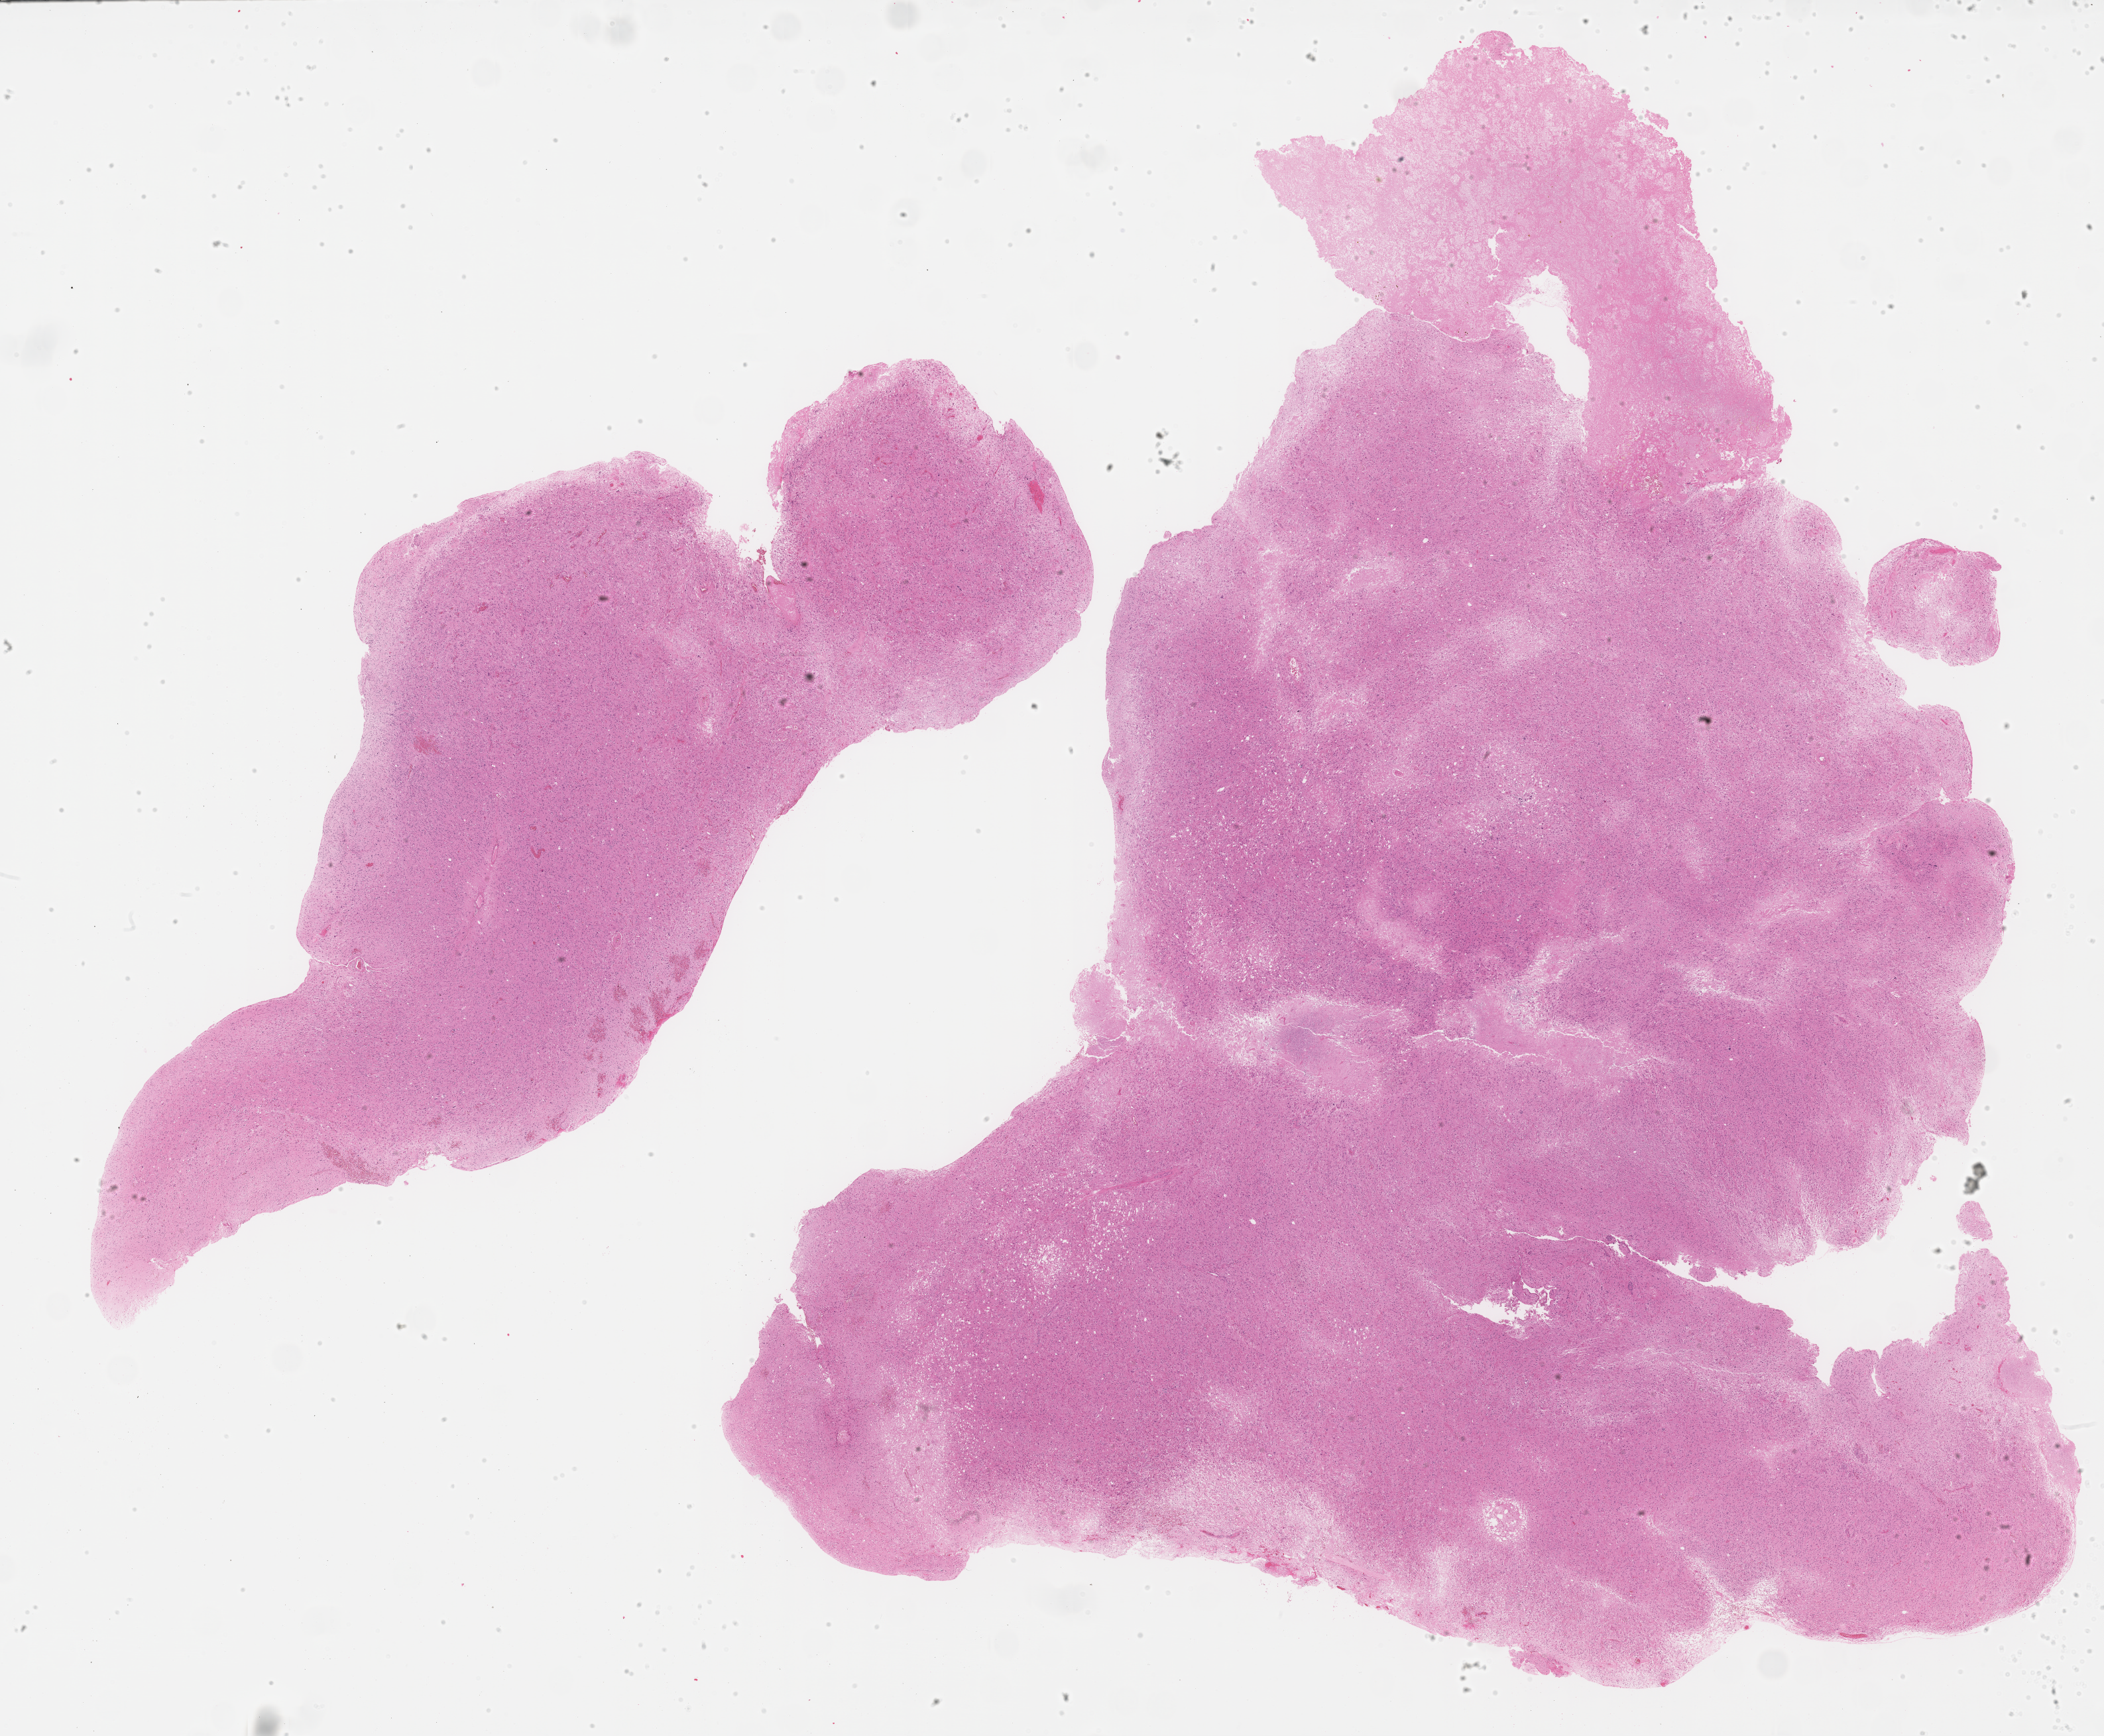
H&E-stained whole-slide image — shown as a low-resolution overview of the whole scanned area (about 25.7 x 21.2 mm, slide scanned at 40x), formalin-fixed paraffin-embedded (FFPE) diagnostic section, brain, primary tumour sample. Patient: female, age at initial diagnosis 28 years.
Histologic diagnosis: Glioblastoma.